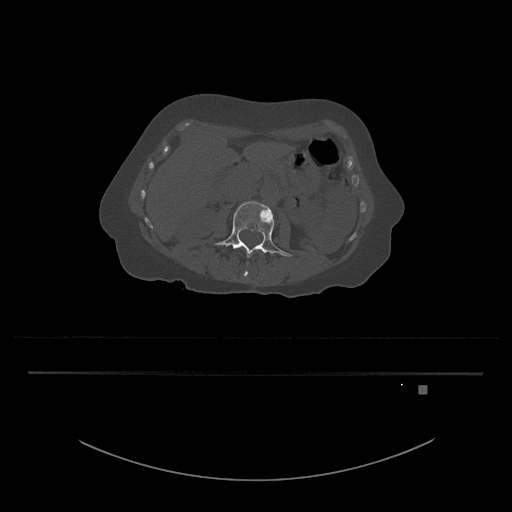
CT including the spine, one axial slice; slice 434 of 797 in the series (ordered by position); reconstruction kernel Br40s/3; bone window (W 1800 / L 400 HU); 0.5 mm slice thickness; 512 × 512 image matrix. Female patient, age 57 years. Case-level facts recorded for this patient, not image findings: primary cancer: cervical.
Structures marked on this image (semi-automatic segmentation, software-assisted and operator-edited):
- L3 vertebra: bounding box <214,201,292,276> (left, top, right, bottom; pixels)